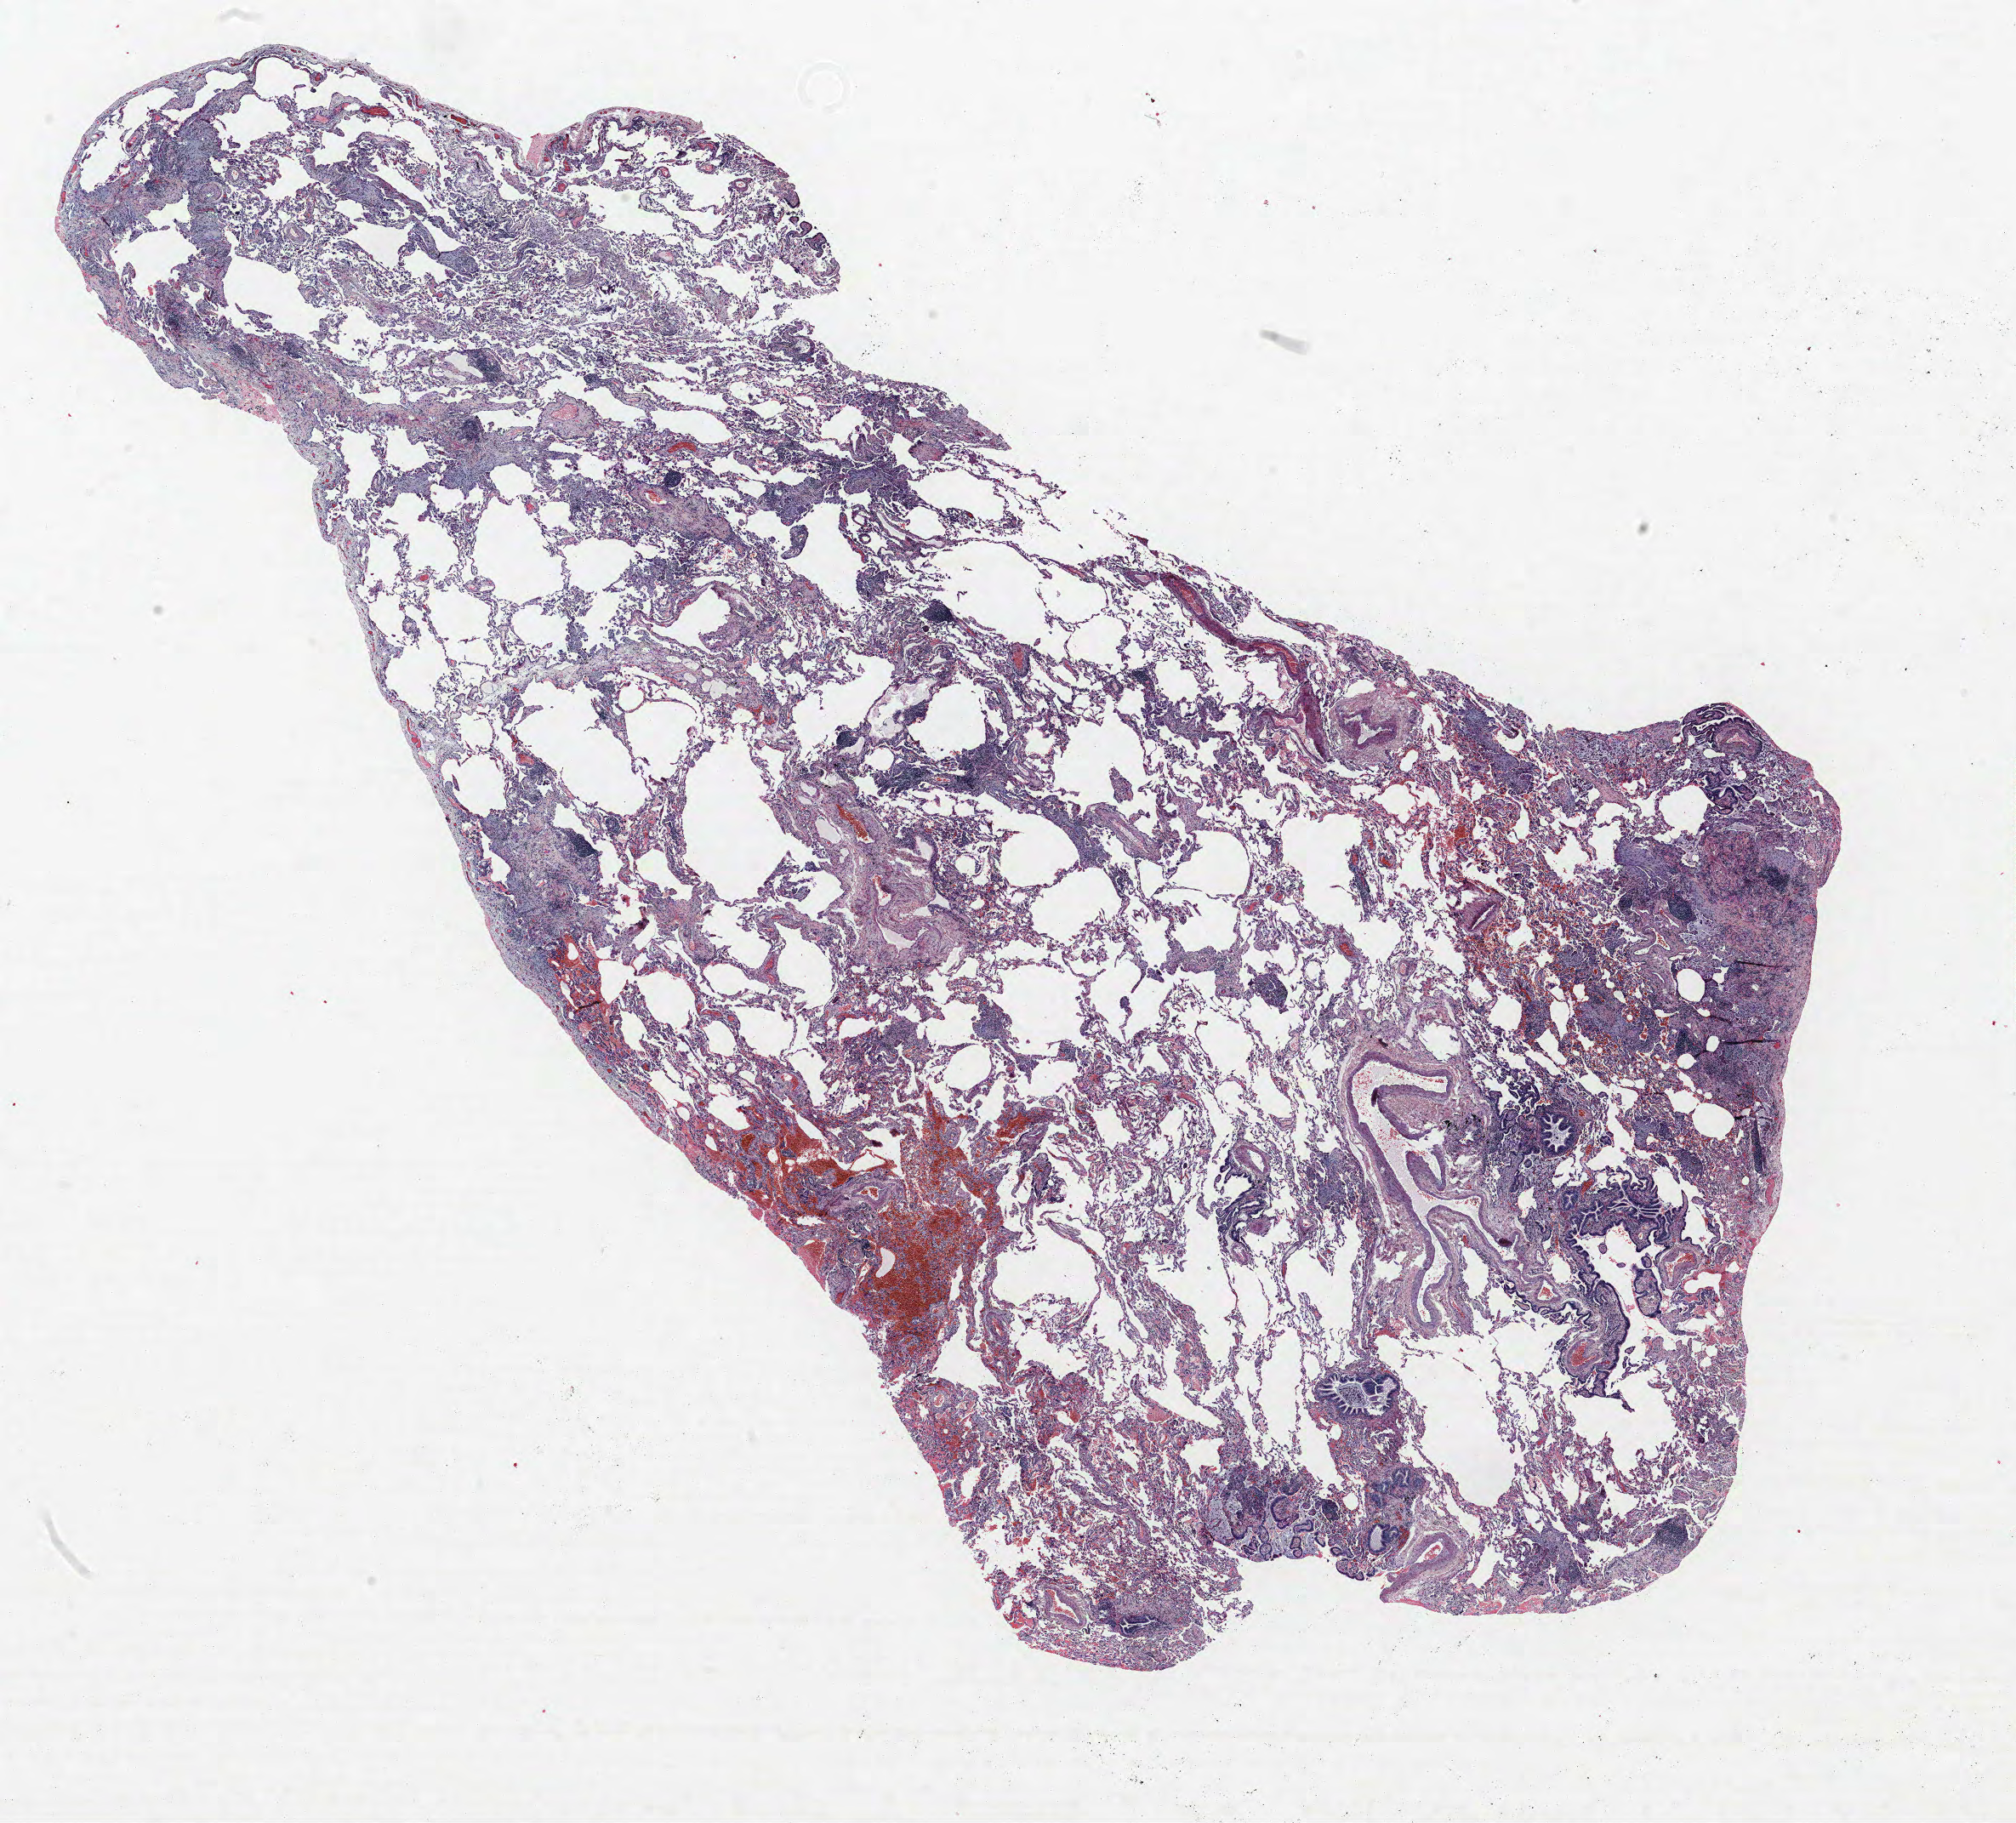
H&E-stained whole-slide image — shown as a low-resolution overview of the whole scanned area (about 19.0 x 17.1 mm, slide scanned at 40x); formalin-fixed paraffin-embedded (FFPE) section; lung. Male patient, aged 73 at enrolment. Grade: poorly differentiated (G3).
• primary tumour location (clinical record): left lower lobe
• participant's lung-cancer diagnosis: Adenocarcinoma, NOS (ICD-O-3 8140/3)
• tumour size (pathology): 12 mm
• stage (AJCC 6th edition): IIA